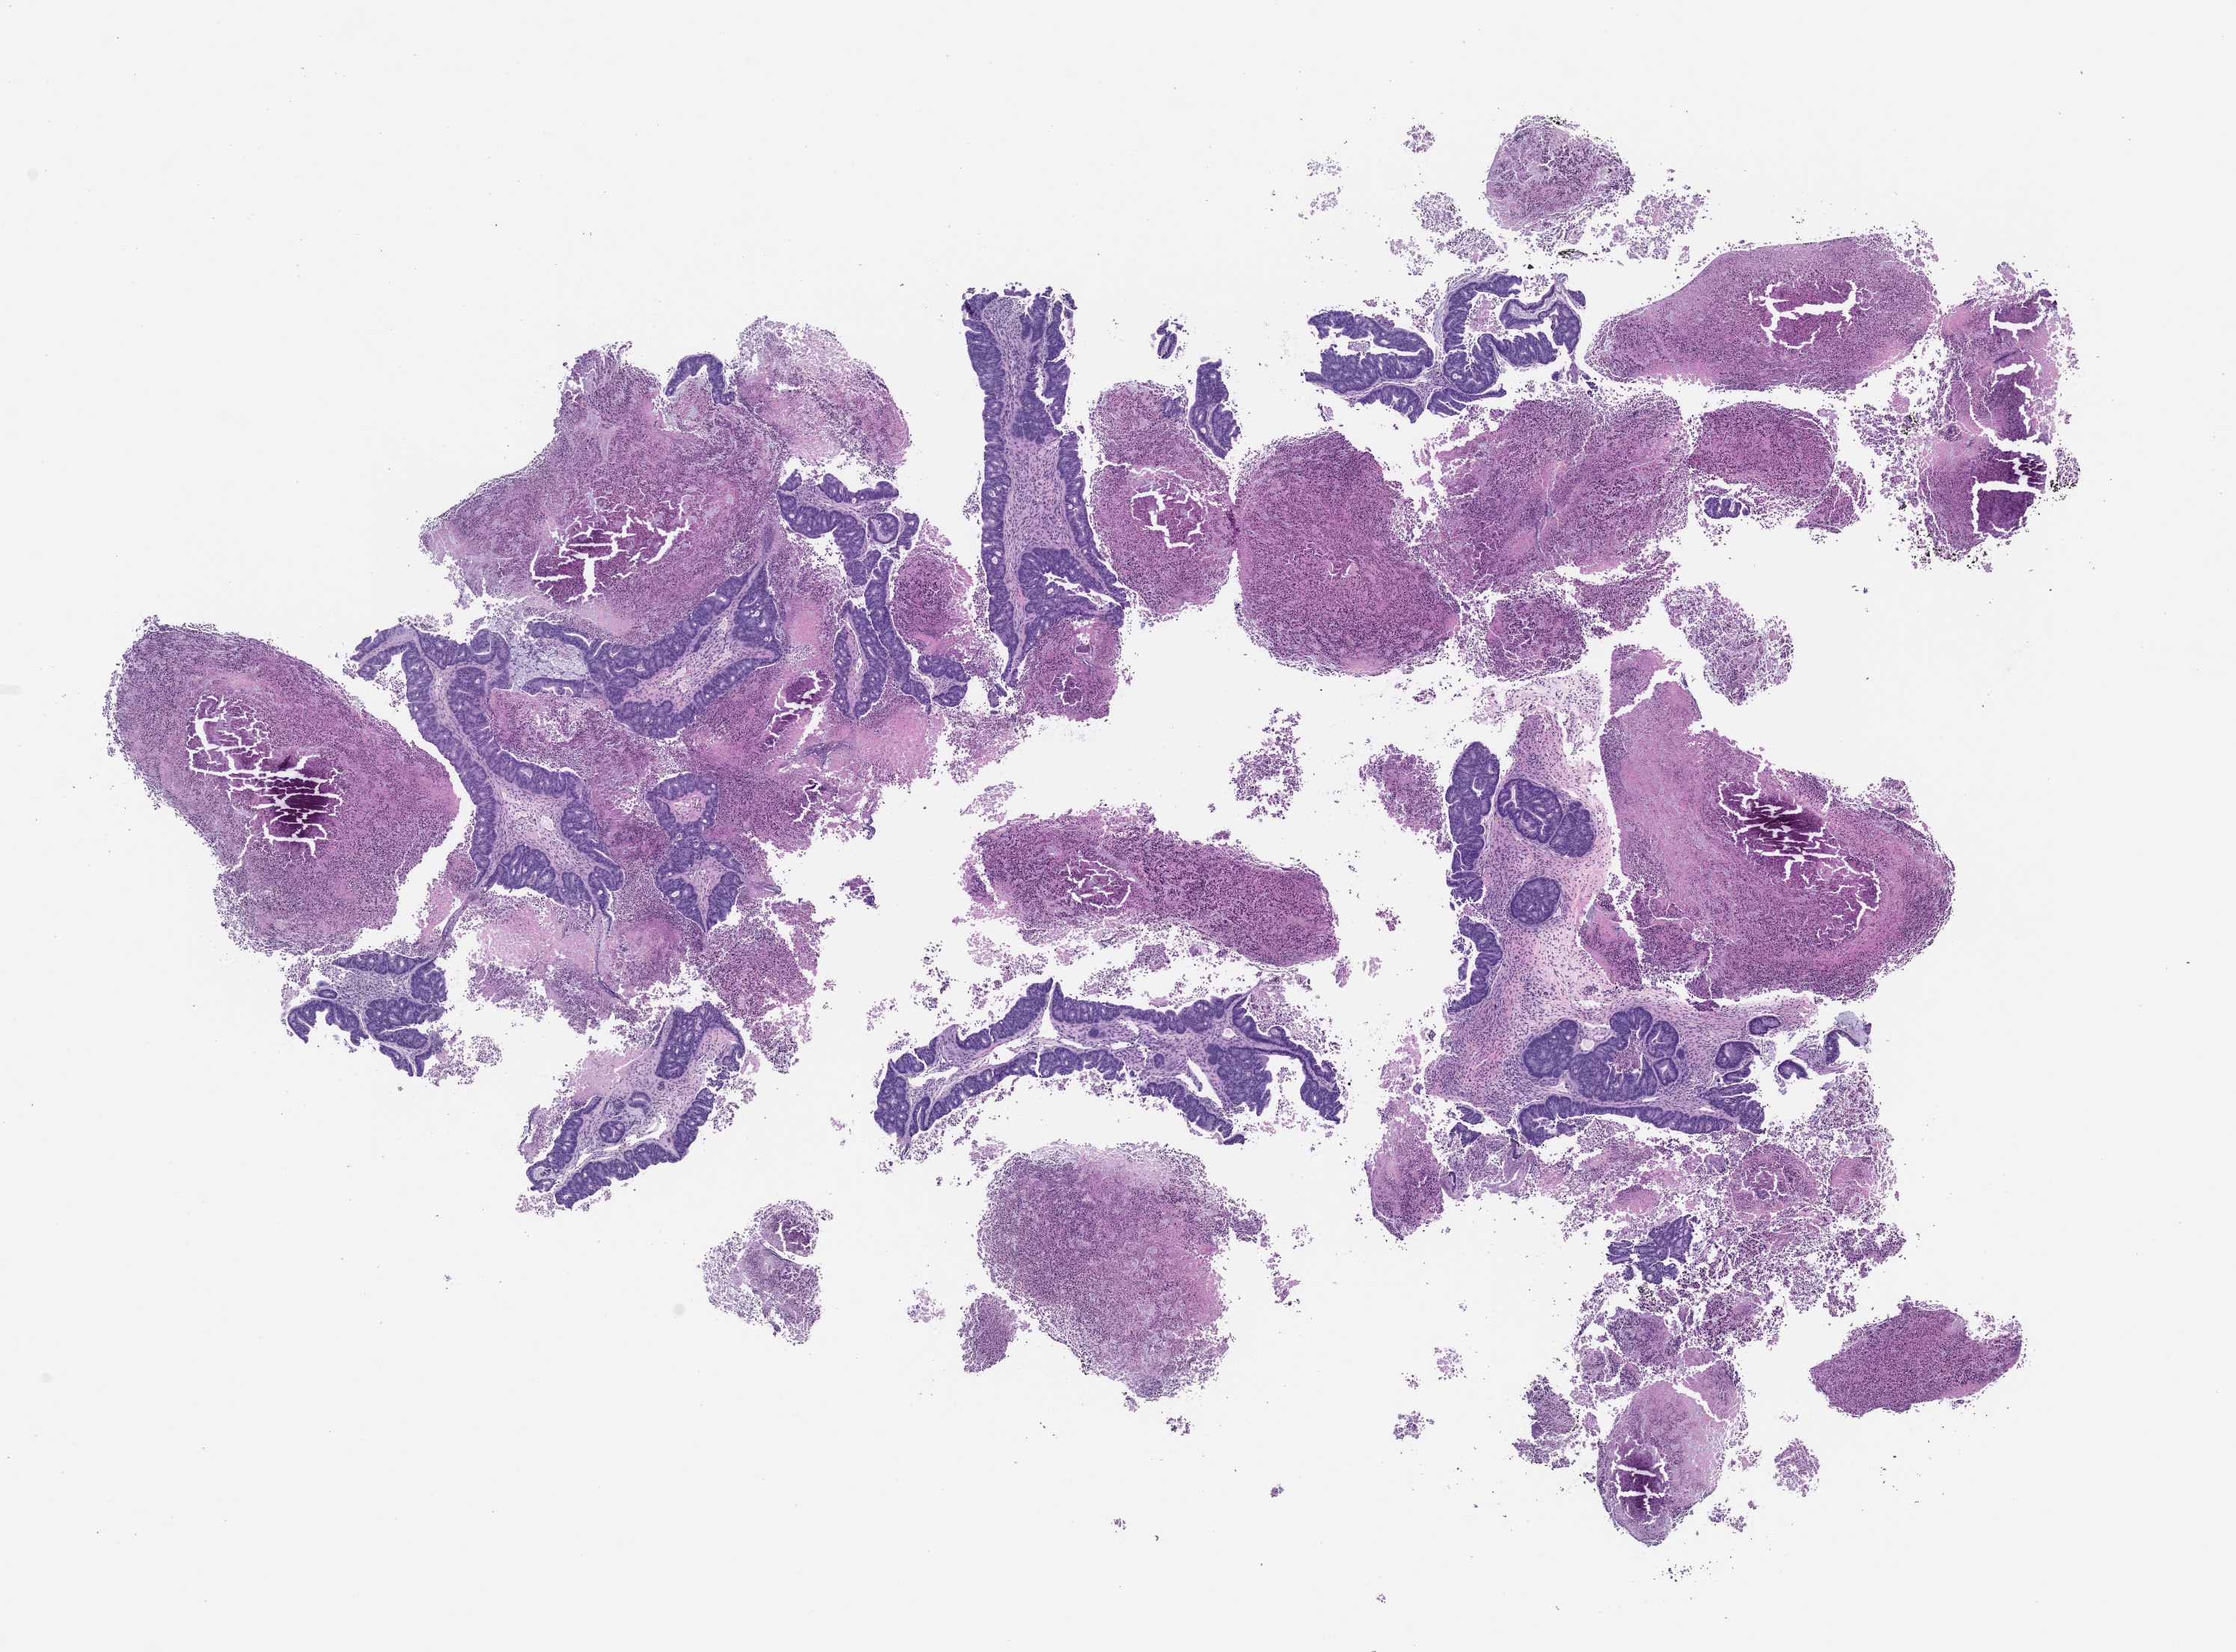
Whole-slide image, hematoxylin and eosin (H&E): patient-derived xenograft (human tumor grown in a mouse), passage 1, whole scanned area (about 12.0 x 8.9 mm) shown as a low-resolution overview. Formalin-fixed, paraffin-embedded (FFPE) tissue. Originating tumor site category: rectum.
Originating patient diagnosis: Rectal Adenocarcinoma.